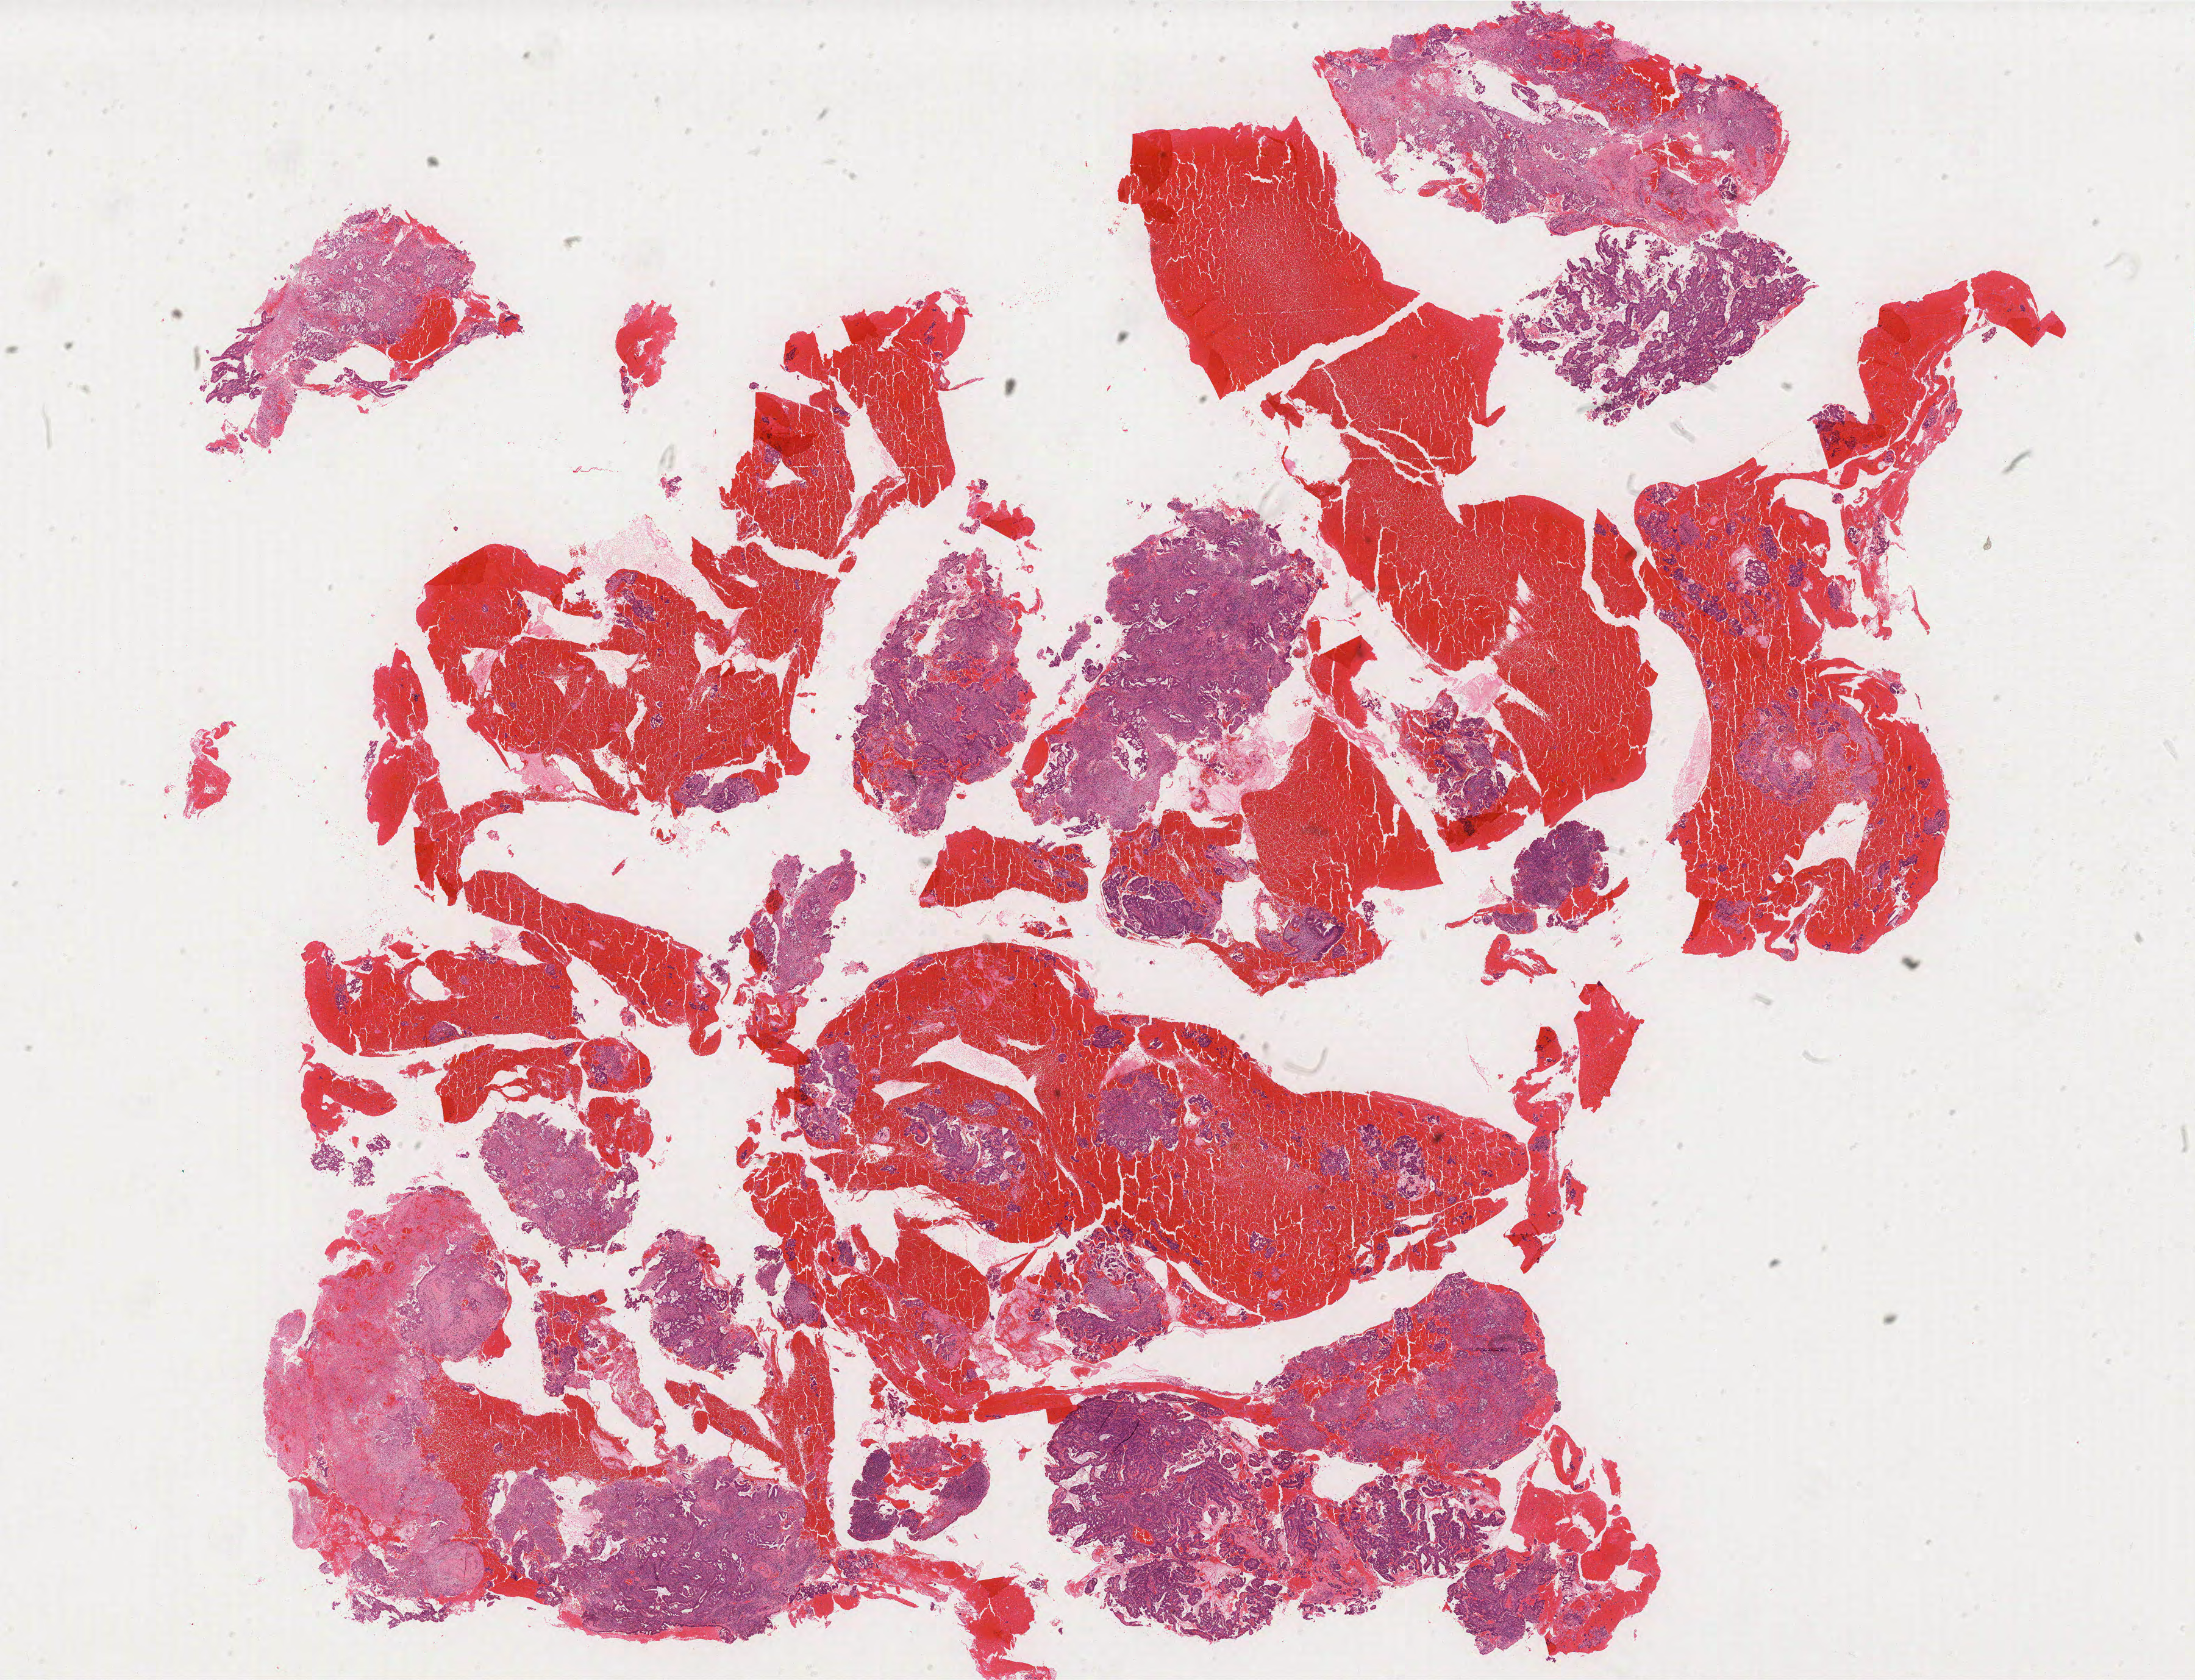
H&E-stained whole-slide image, low-resolution overview of the scanned area, about 28.8 x 22.1 mm. Formalin-fixed paraffin-embedded (FFPE) diagnostic section. Cervix, primary tumour sample. Female, age 56 years at initial diagnosis. Histologic grade: G2 (moderately differentiated).
- FIGO stage: IB2
- histologic diagnosis: Adenocarcinoma, NOS (cervix uteri)